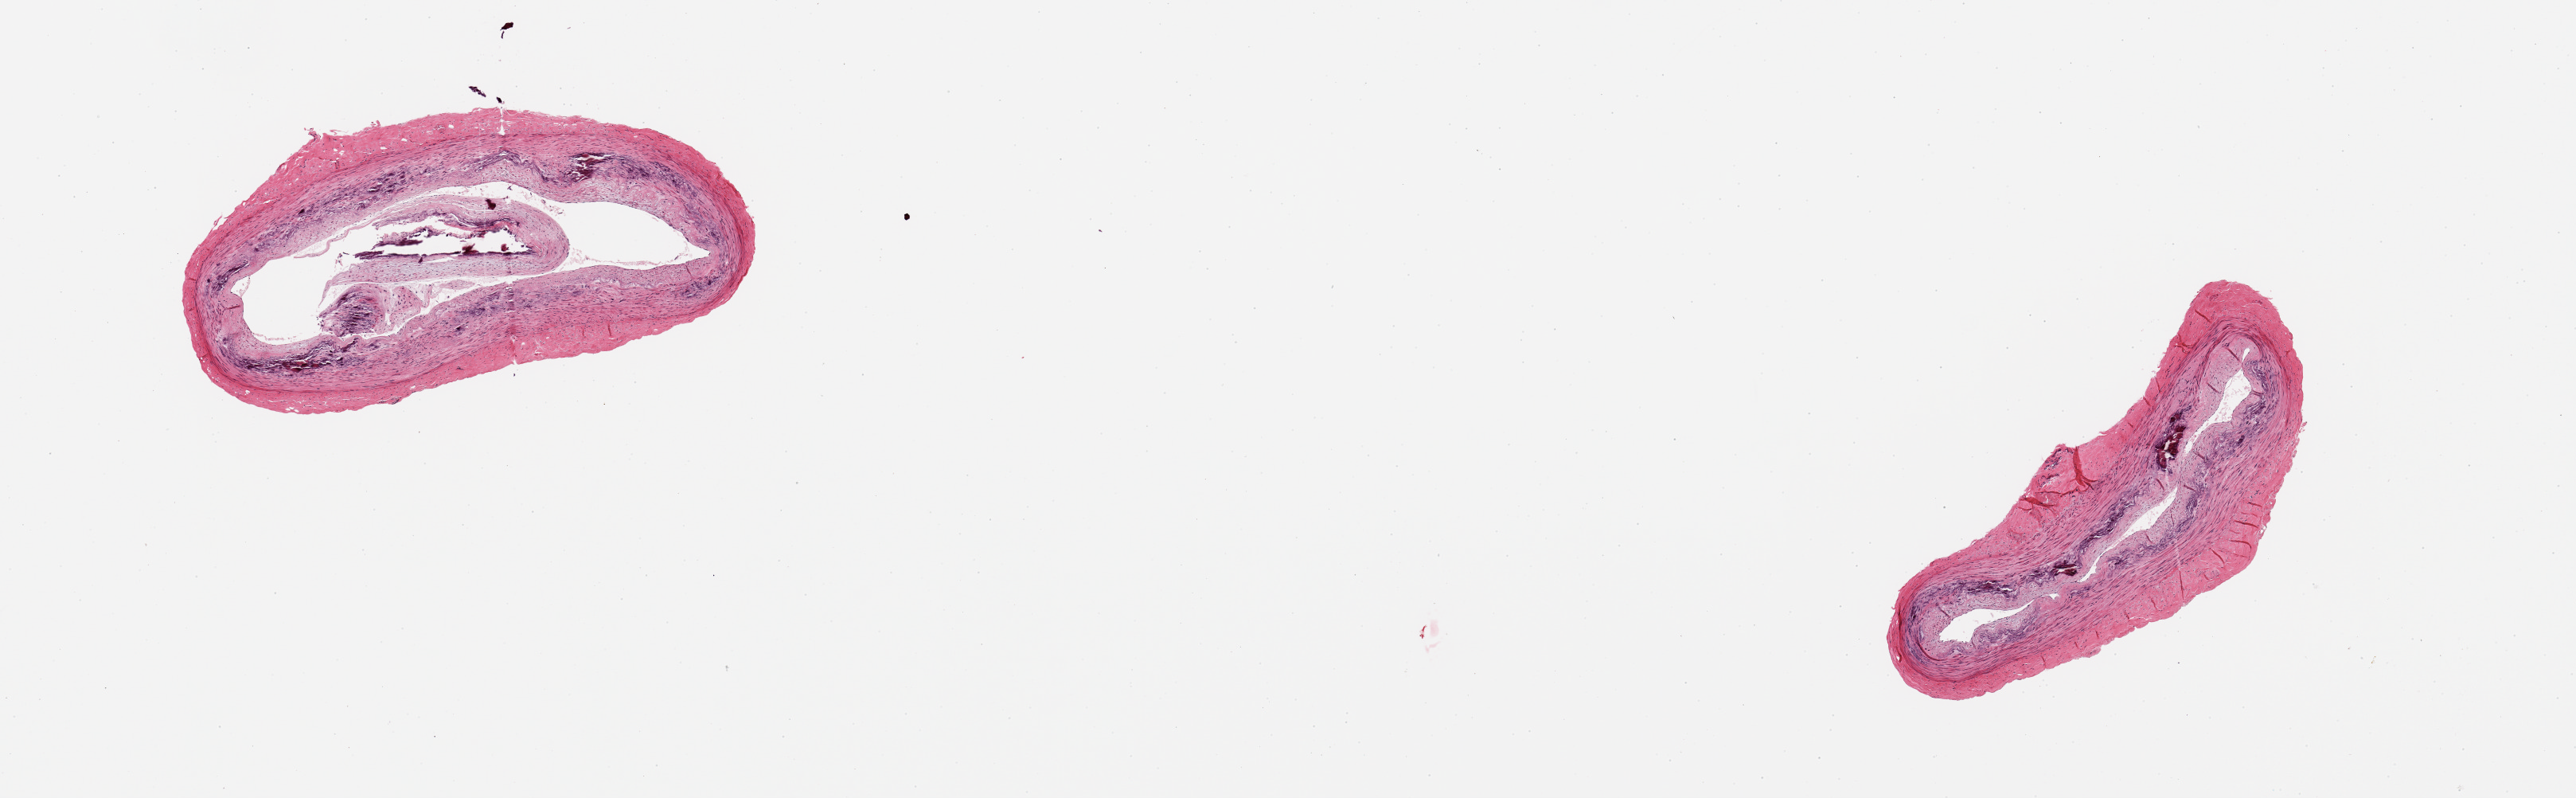
Digitized H&E-stained section, shown as a low-resolution overview of the whole scanned area (about 12.8 x 4.0 mm, from a 20x scan); PAXgene-fixed, paraffin-embedded tissue; sampled site (target tissue): tibial artery; donor tissue sample. Donor sex: female.
Pathologist's review note for this sample: 2 pieces, prominent Monckeberg medial sclerosis; Minimal atherosis/adherent fat.